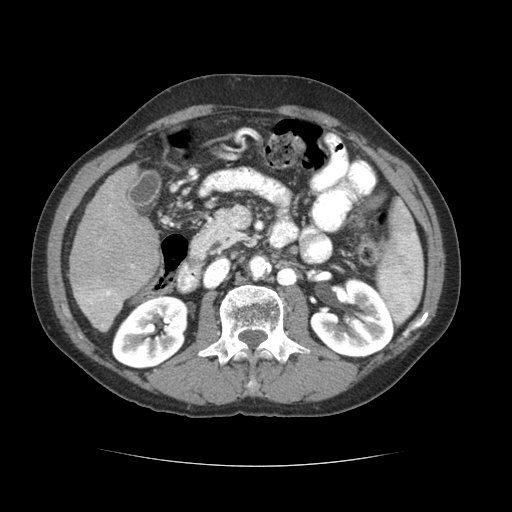
Contrast-enhanced abdominal CT (liver protocol), one axial slice; soft-tissue window (W 400 / L 40 HU); 2.5 mm slice thickness; 512 × 512 image matrix. From the clinical record (not read from this slice): diagnosis: hepatocellular carcinoma (patient treated with transarterial chemoembolisation; whether this scan precedes or follows treatment is not stated here); TNM stage (as recorded): Stage-II; Child-Pugh class: B; tumour differentiation: poorly differentiated.
Outlined on this slice (semi-automatic segmentation, software-assisted and operator-edited):
- liver parenchyma outside the tumour (the mass and vessels are separate outlines, so this box may not span the whole liver): bounding box [x1, y1, x2, y2] px = [68, 164, 160, 331]
- liver vessels: [76, 264, 135, 327]